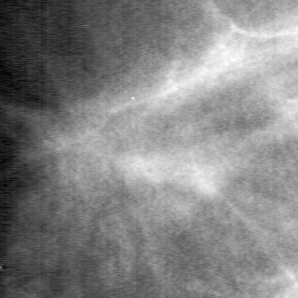
Region of interest cut from a scanned film mammogram (one marked finding); left breast; MLO view.
Finding: mass, shape irregular, margins spiculated; BI-RADS assessment category 5; pathology result (as recorded, not read from the image): malignant.